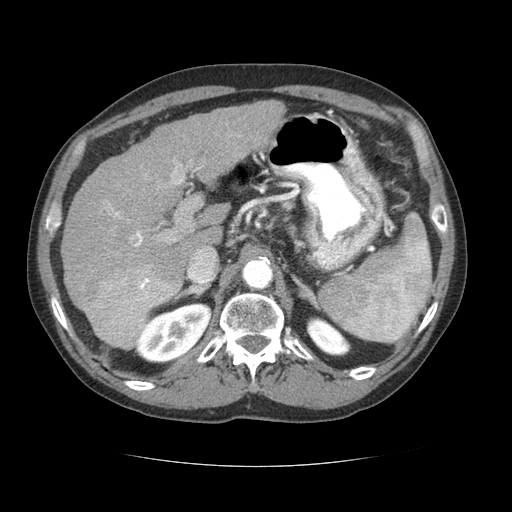
Contrast-enhanced abdominal CT (liver protocol), one axial slice. Slice 46 of 69 in the series (ordered by position). 120 kVp. Soft-tissue window (W 400 / L 40 HU). 512 × 512 image matrix, field of view 360 × 360 mm. Case-level facts recorded for this patient, not image findings: diagnosis: hepatocellular carcinoma (patient treated with transarterial chemoembolisation; whether this scan precedes or follows treatment is not stated here); TNM stage (as recorded): Stage-II.
Outlined on this slice (semi-automatic segmentation, software-assisted and operator-edited):
- liver parenchyma outside the tumour (the mass and vessels are separate outlines, so this box may not span the whole liver): bounding box <60,100,284,320> (left, top, right, bottom; pixels)
- mass: <85,263,180,352>
- liver vessels: <109,160,216,290>